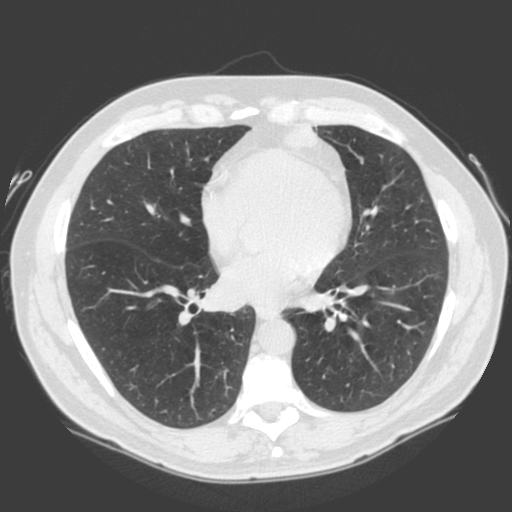
Low-dose screening chest CT, one axial slice; slice 84 of 185 in the series (ordered by position); 120 kVp; lung window (W 1500 / L -600 HU); 2 mm slice thickness; 512 × 512 image matrix, field of view 360 × 360 mm.
Annotated regions visible in this slice (manually delineated by an expert):
- lesion 1 (tumor, lower lobe of left lung): box from (x=283, y=123) to (x=336, y=165) px